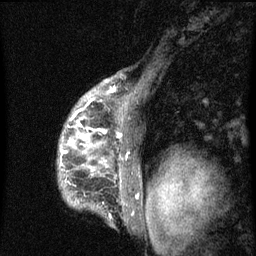
Breast MRI (dynamic contrast-enhanced), one sagittal slice. Slice 50 of 60 in the series (ordered by position). Dynamic contrast-enhanced series, image 2 of 3 at this slice position (ordered by acquisition). 1.5 T. TE 4.2 ms, TR 8 ms. 256 × 256 image matrix, field of view 190 × 190 mm. Patient: female, 50 years.
Annotated regions visible in this slice (semi-automatic segmentation, software-assisted and operator-edited):
- analysis volume of interest (the breast-tissue region the enhancement analysis was run in; not a lesion): box from (x=58, y=90) to (x=142, y=216) px
- tumour enhancement mask (voxels above the 70 % enhancement threshold inside the analysis volume of interest): (x=60, y=92)–(x=121, y=175)